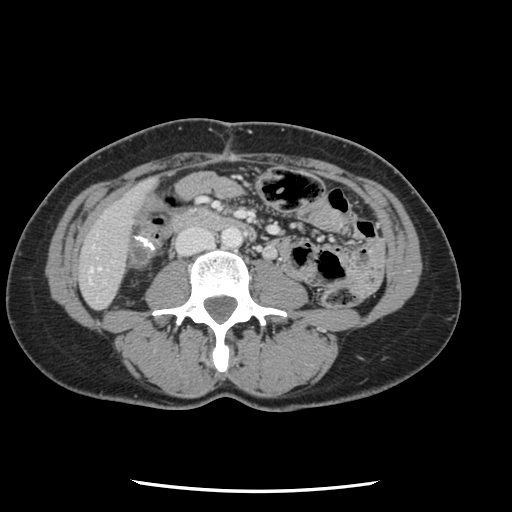
Contrast-enhanced abdominal CT, one axial slice; slice 15 of 134 in the series (ordered by position); intravenous contrast given; soft-tissue window (W 400 / L 40 HU); 2.5 mm slice thickness; 512 × 512 image matrix, field of view 330 × 330 mm. Female patient, age 43 years. From the clinical record (not read from this slice): diagnosis: colorectal cancer liver metastases, imaged before liver resection; multiple liver metastases: yes; largest metastasis: 3.4 cm; chemotherapy before resection: no.
Structures marked on this image (manually delineated by an expert):
- hepatic veins: bounding box (x1, y1, x2, y2) in pixels: (90, 269, 92, 272)
- liver: (80, 184, 148, 308)
- planned liver remnant (the part of the liver to remain after resection): (80, 184, 149, 308)